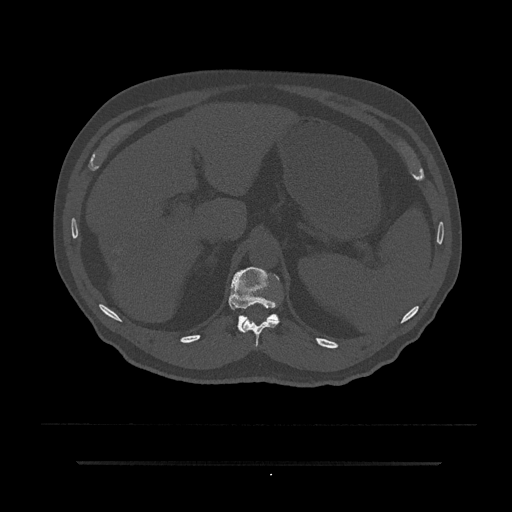
CT including the spine, one axial slice; slice 240 of 797 in the series (ordered by position); 120 kVp; bone window (W 1800 / L 400 HU); 0.5 mm slice thickness; 512 × 512 image matrix, field of view 464 × 464 mm. Male patient, age 59 years. Case-level facts recorded for this patient, not image findings: primary cancer: bile ducts; vertebrae with lytic lesions (as recorded): T10.
Outlined on this slice (semi-automatically segmented with operator editing):
- T11 vertebra: bounding box (x1, y1, x2, y2) in pixels: (242, 319, 280, 347)
- T12 vertebra: (229, 267, 279, 333)